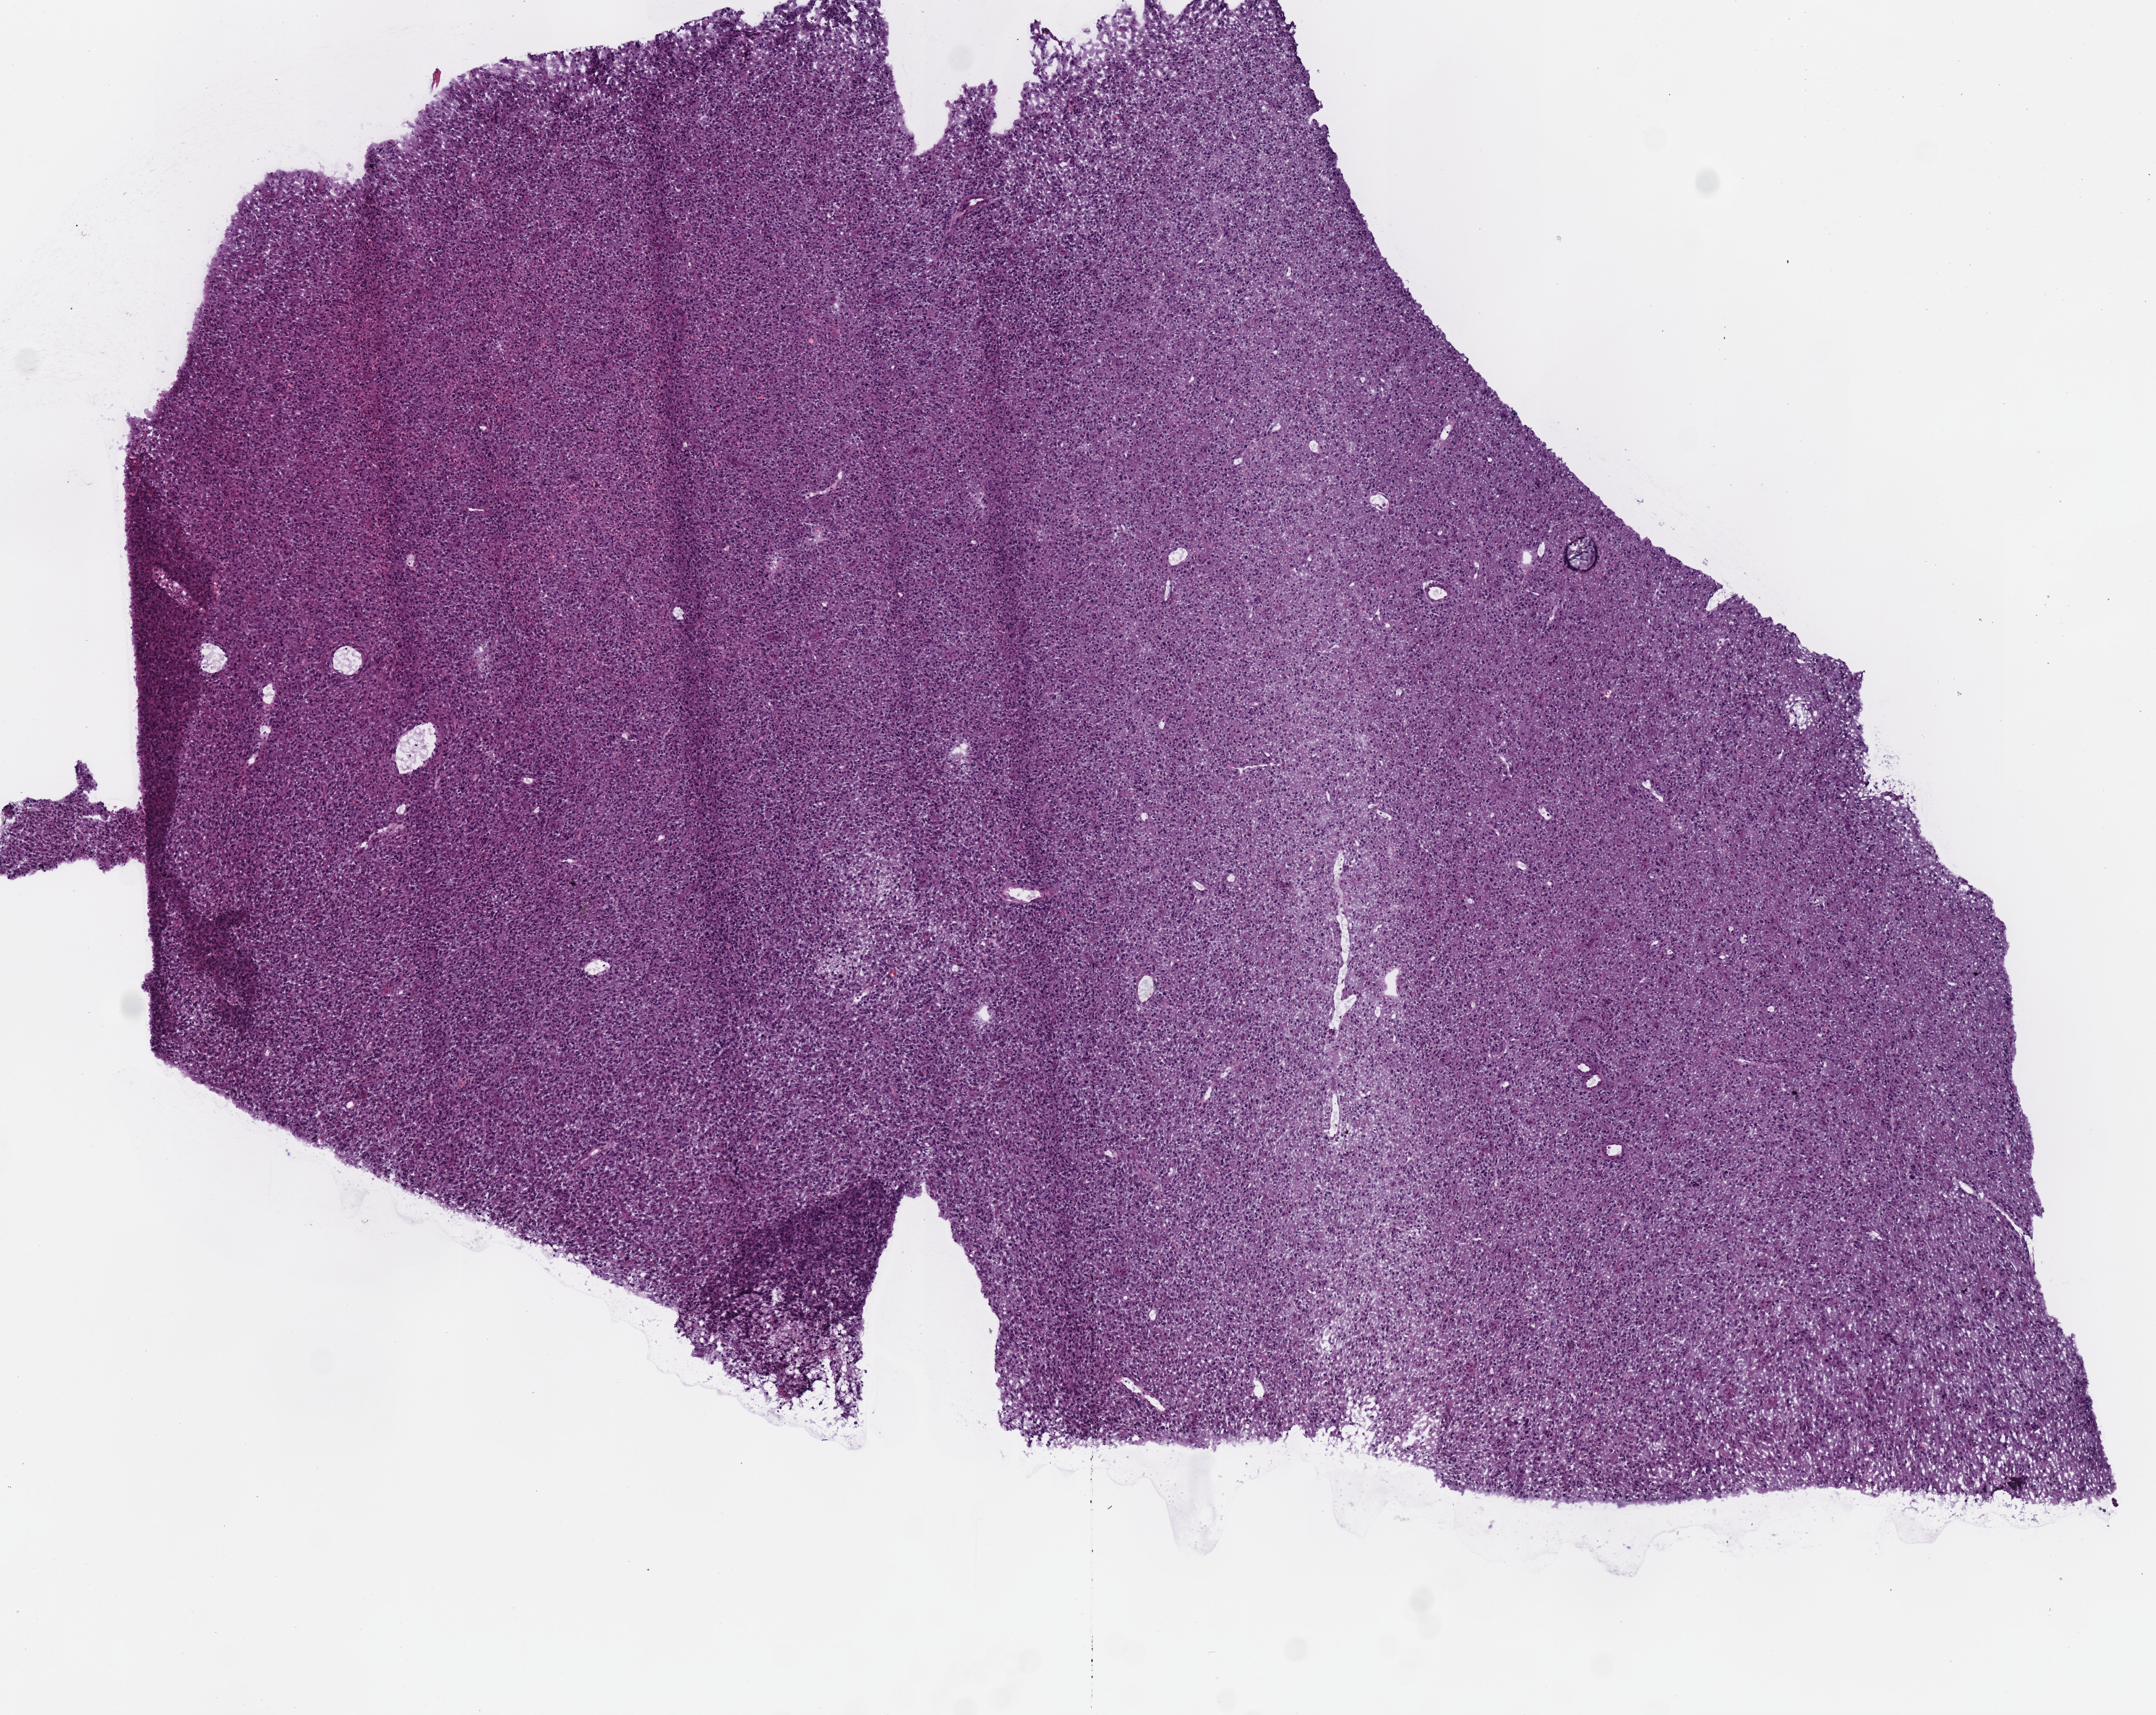
Whole-slide histology image, H&E-stained, whole scanned area (about 6.9 x 5.5 mm) shown as a low-resolution overview. Frozen section. Brain, primary tumour sample. Patient: female, age at initial diagnosis 51 years. Histologic grade: G3 (poorly differentiated). Slide review estimates, as recorded: tumour cells 100%, tumour nuclei 75%, normal cells 0%, stromal cells 0%, necrosis 0%.
Pathologic diagnosis: Astrocytoma, anaplastic (cerebrum).